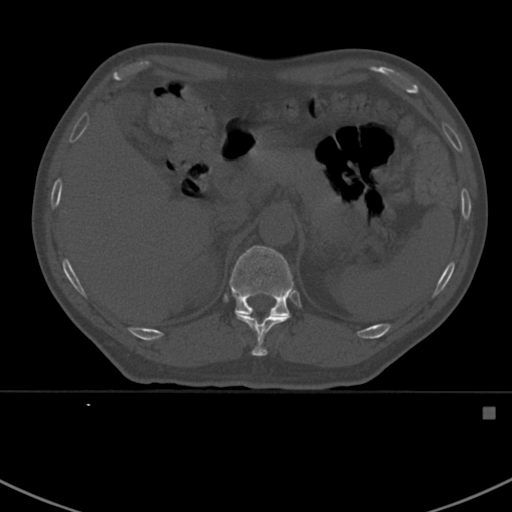
CT including the spine, one axial slice. Slice 338 of 412 in the series (ordered by position). Reconstruction kernel Br40s. 120 kVp. Bone window (W 1800 / L 400 HU). 512 × 512 image matrix, field of view 358 × 358 mm. Male patient, age 59 years. Case-level facts recorded for this patient, not image findings: primary cancer: prostate.
Annotated regions visible in this slice (semi-automatic segmentation, software-assisted and operator-edited):
- T11 vertebra: bounding box [x1, y1, x2, y2] px = [236, 314, 289, 356]
- T12 vertebra: [230, 245, 293, 317]